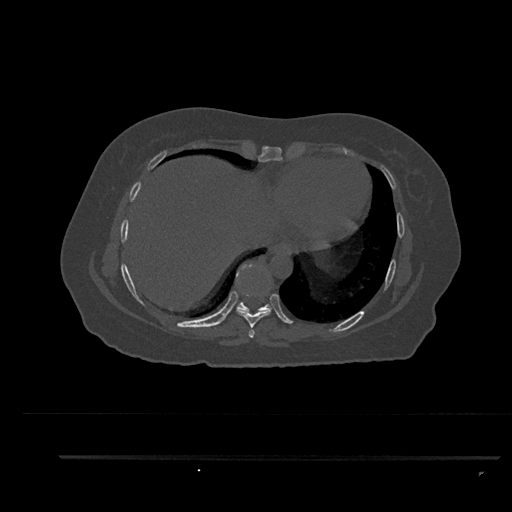
CT including the spine, one axial slice. Slice 443 of 797 in the series (ordered by position). 120 kVp. Bone window (W 1800 / L 400 HU). 0.5 mm slice thickness. 512 × 512 image matrix, field of view 408 × 408 mm. Patient: female, 44 years. From the clinical record (not read from this slice): primary cancer: renal.
Outlined on this slice (semi-automatic segmentation, software-assisted and operator-edited):
- T7 vertebra: bounding box (x1, y1, x2, y2) in pixels: (248, 329, 255, 338)
- T8 vertebra: (236, 293, 271, 328)
- T9 vertebra: (236, 263, 272, 313)